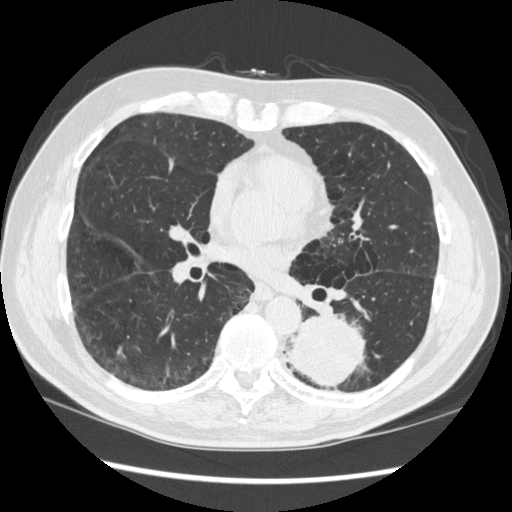
Low-dose screening chest CT, axial slice. First (baseline) screen. Lung window (W 1500 / L -600 HU). Standard (soft-tissue) reconstruction kernel (STANDARD). Male, age 72 years at enrolment.
Lesion marked by an expert reader, bounding box <266,304,370,396> (left, top, right, bottom; pixels). The screening reader recorded 2 non-calcified nodules or masses ≥4 mm on this exam (left lower lobe, right middle lobe); which of them this box marks is not recorded. Official screen result: positive, change unspecified: nodule(s) >= 4 mm or enlarging nodule(s), mass(es), or other non-specific abnormalities suspicious for lung cancer. Later outcome: lung cancer diagnosed 37 days after this screen — squamous cell carcinoma, NOS, left lower lobe, stage IIIA (AJCC 6th edition), 60 mm at pathology.